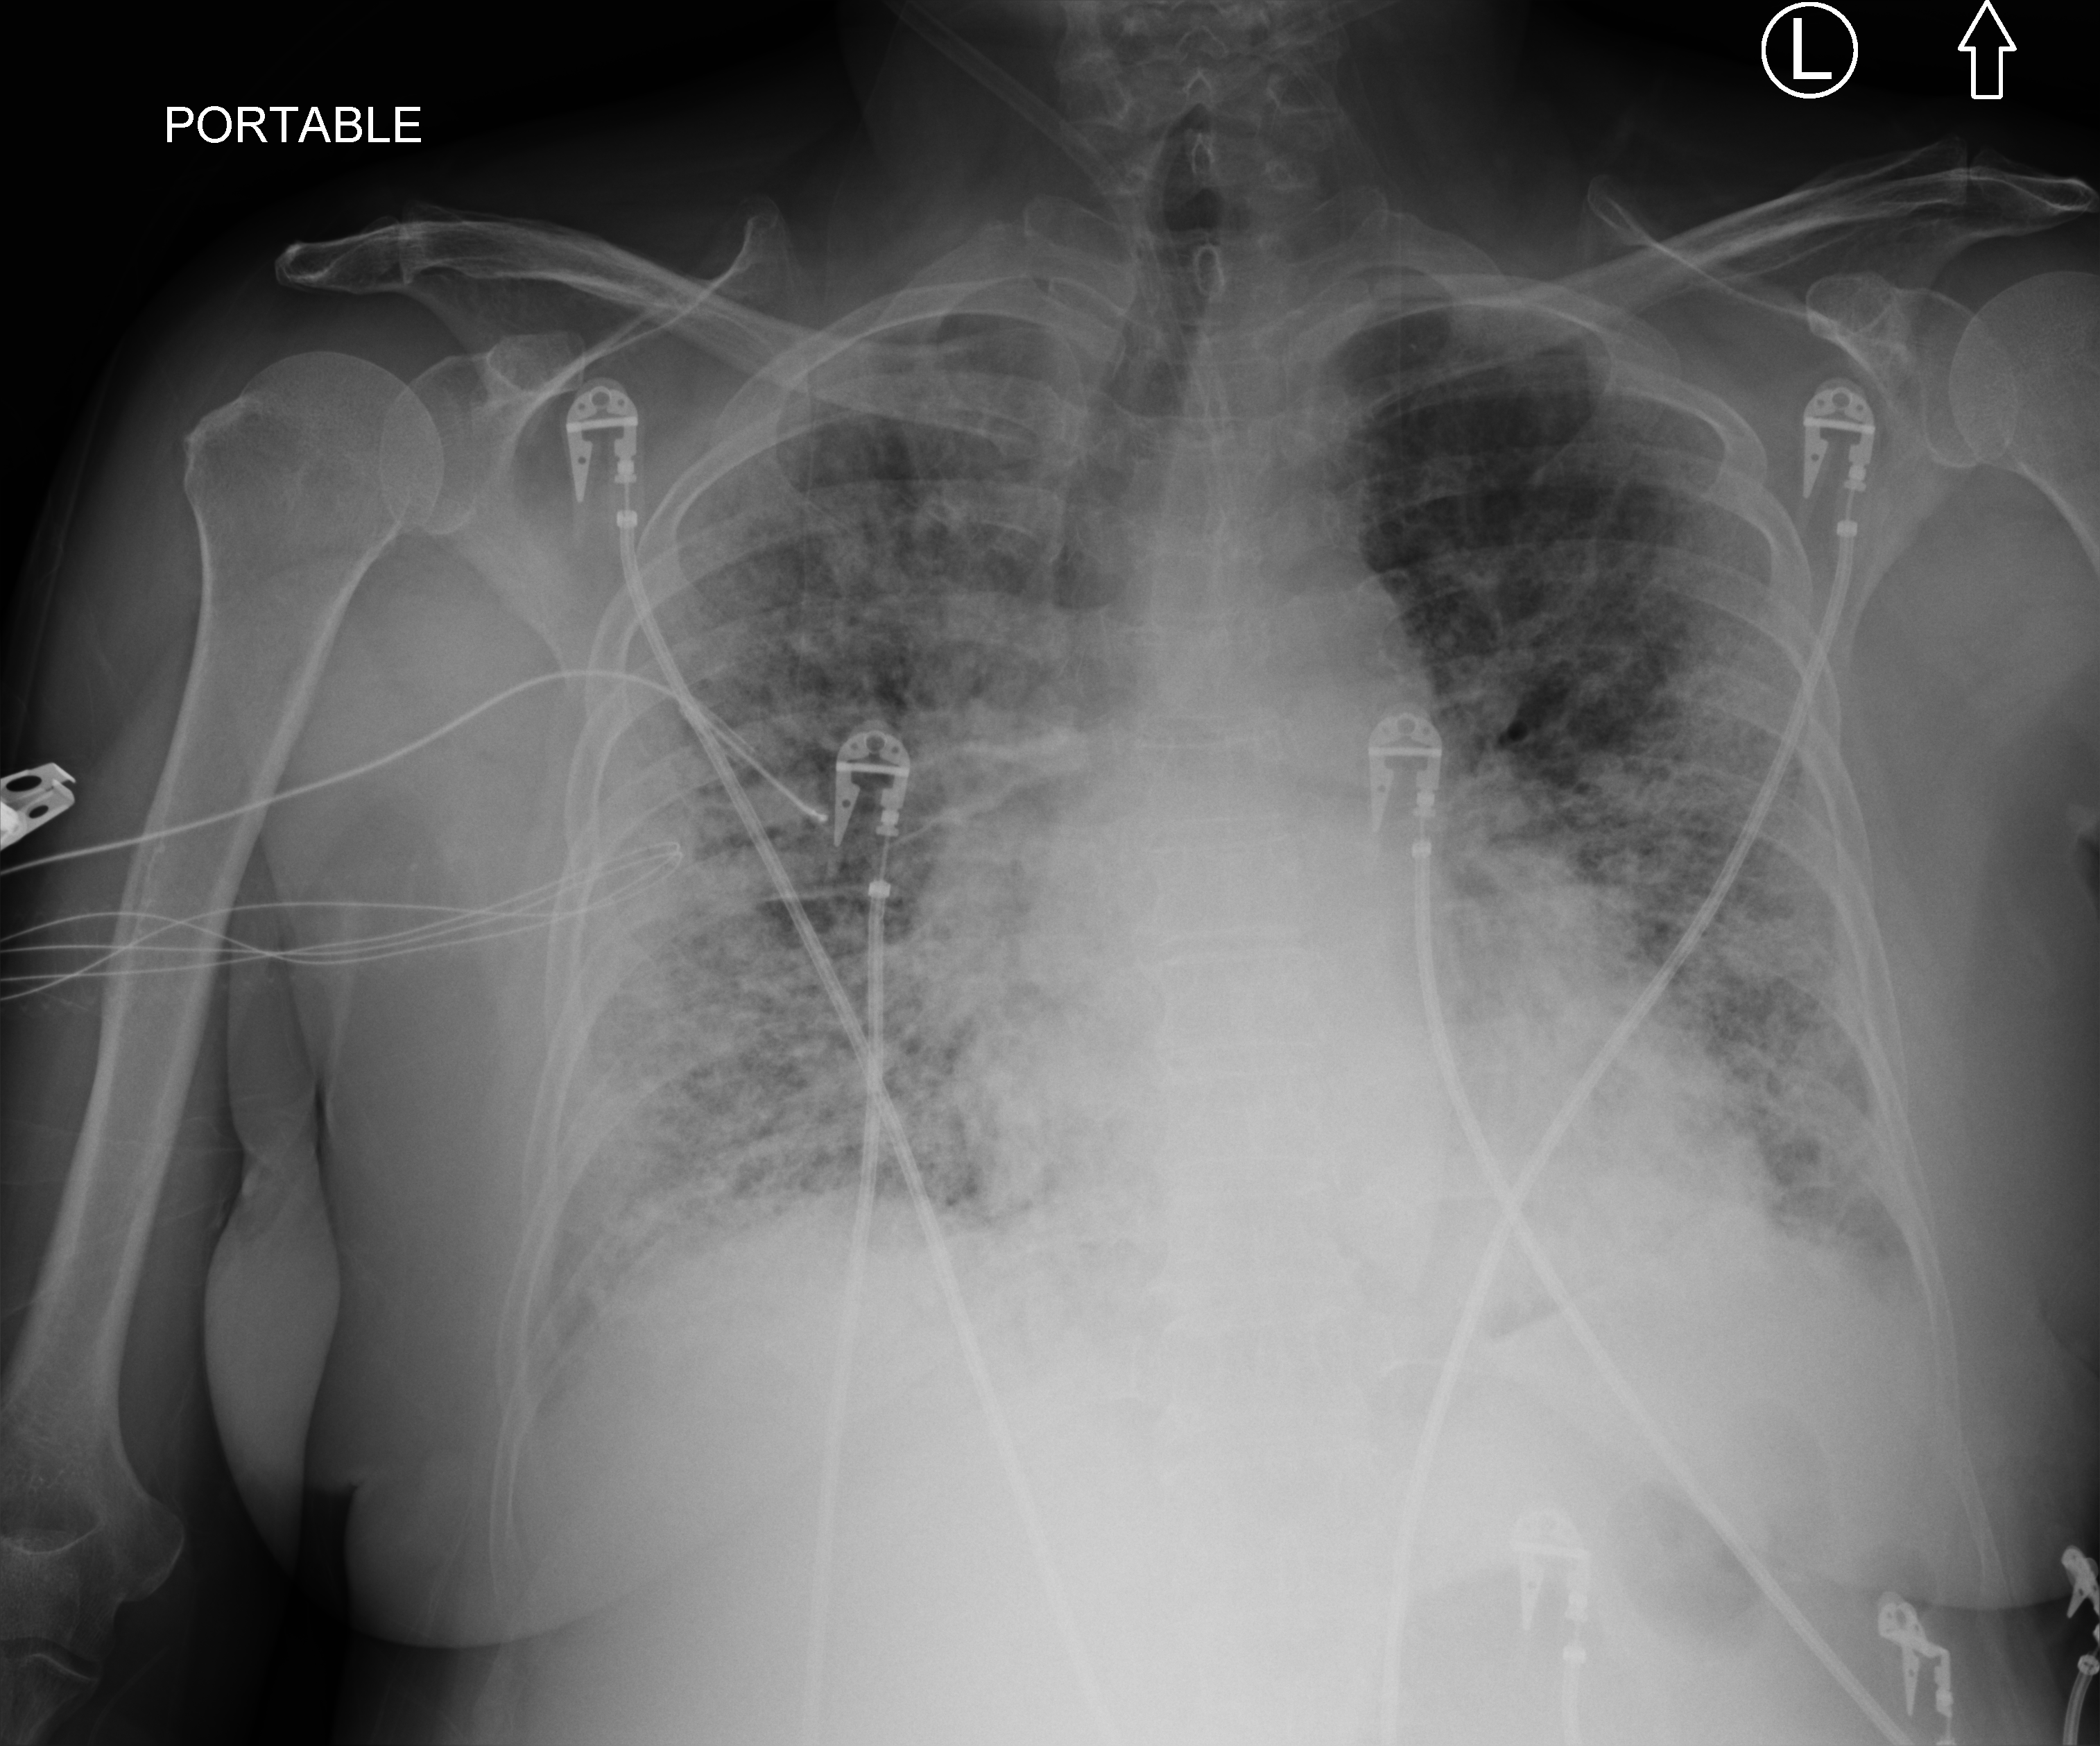
Portable chest radiograph, anteroposterior (AP) projection. Female patient hospitalised with COVID-19, age 60–74 years.
Admission-level facts for this patient (not findings on this image; timing relative to this image not recorded): mechanically ventilated during this hospital stay: yes; smoking status (admission record): never; other chronic lung disease (admission record): yes.